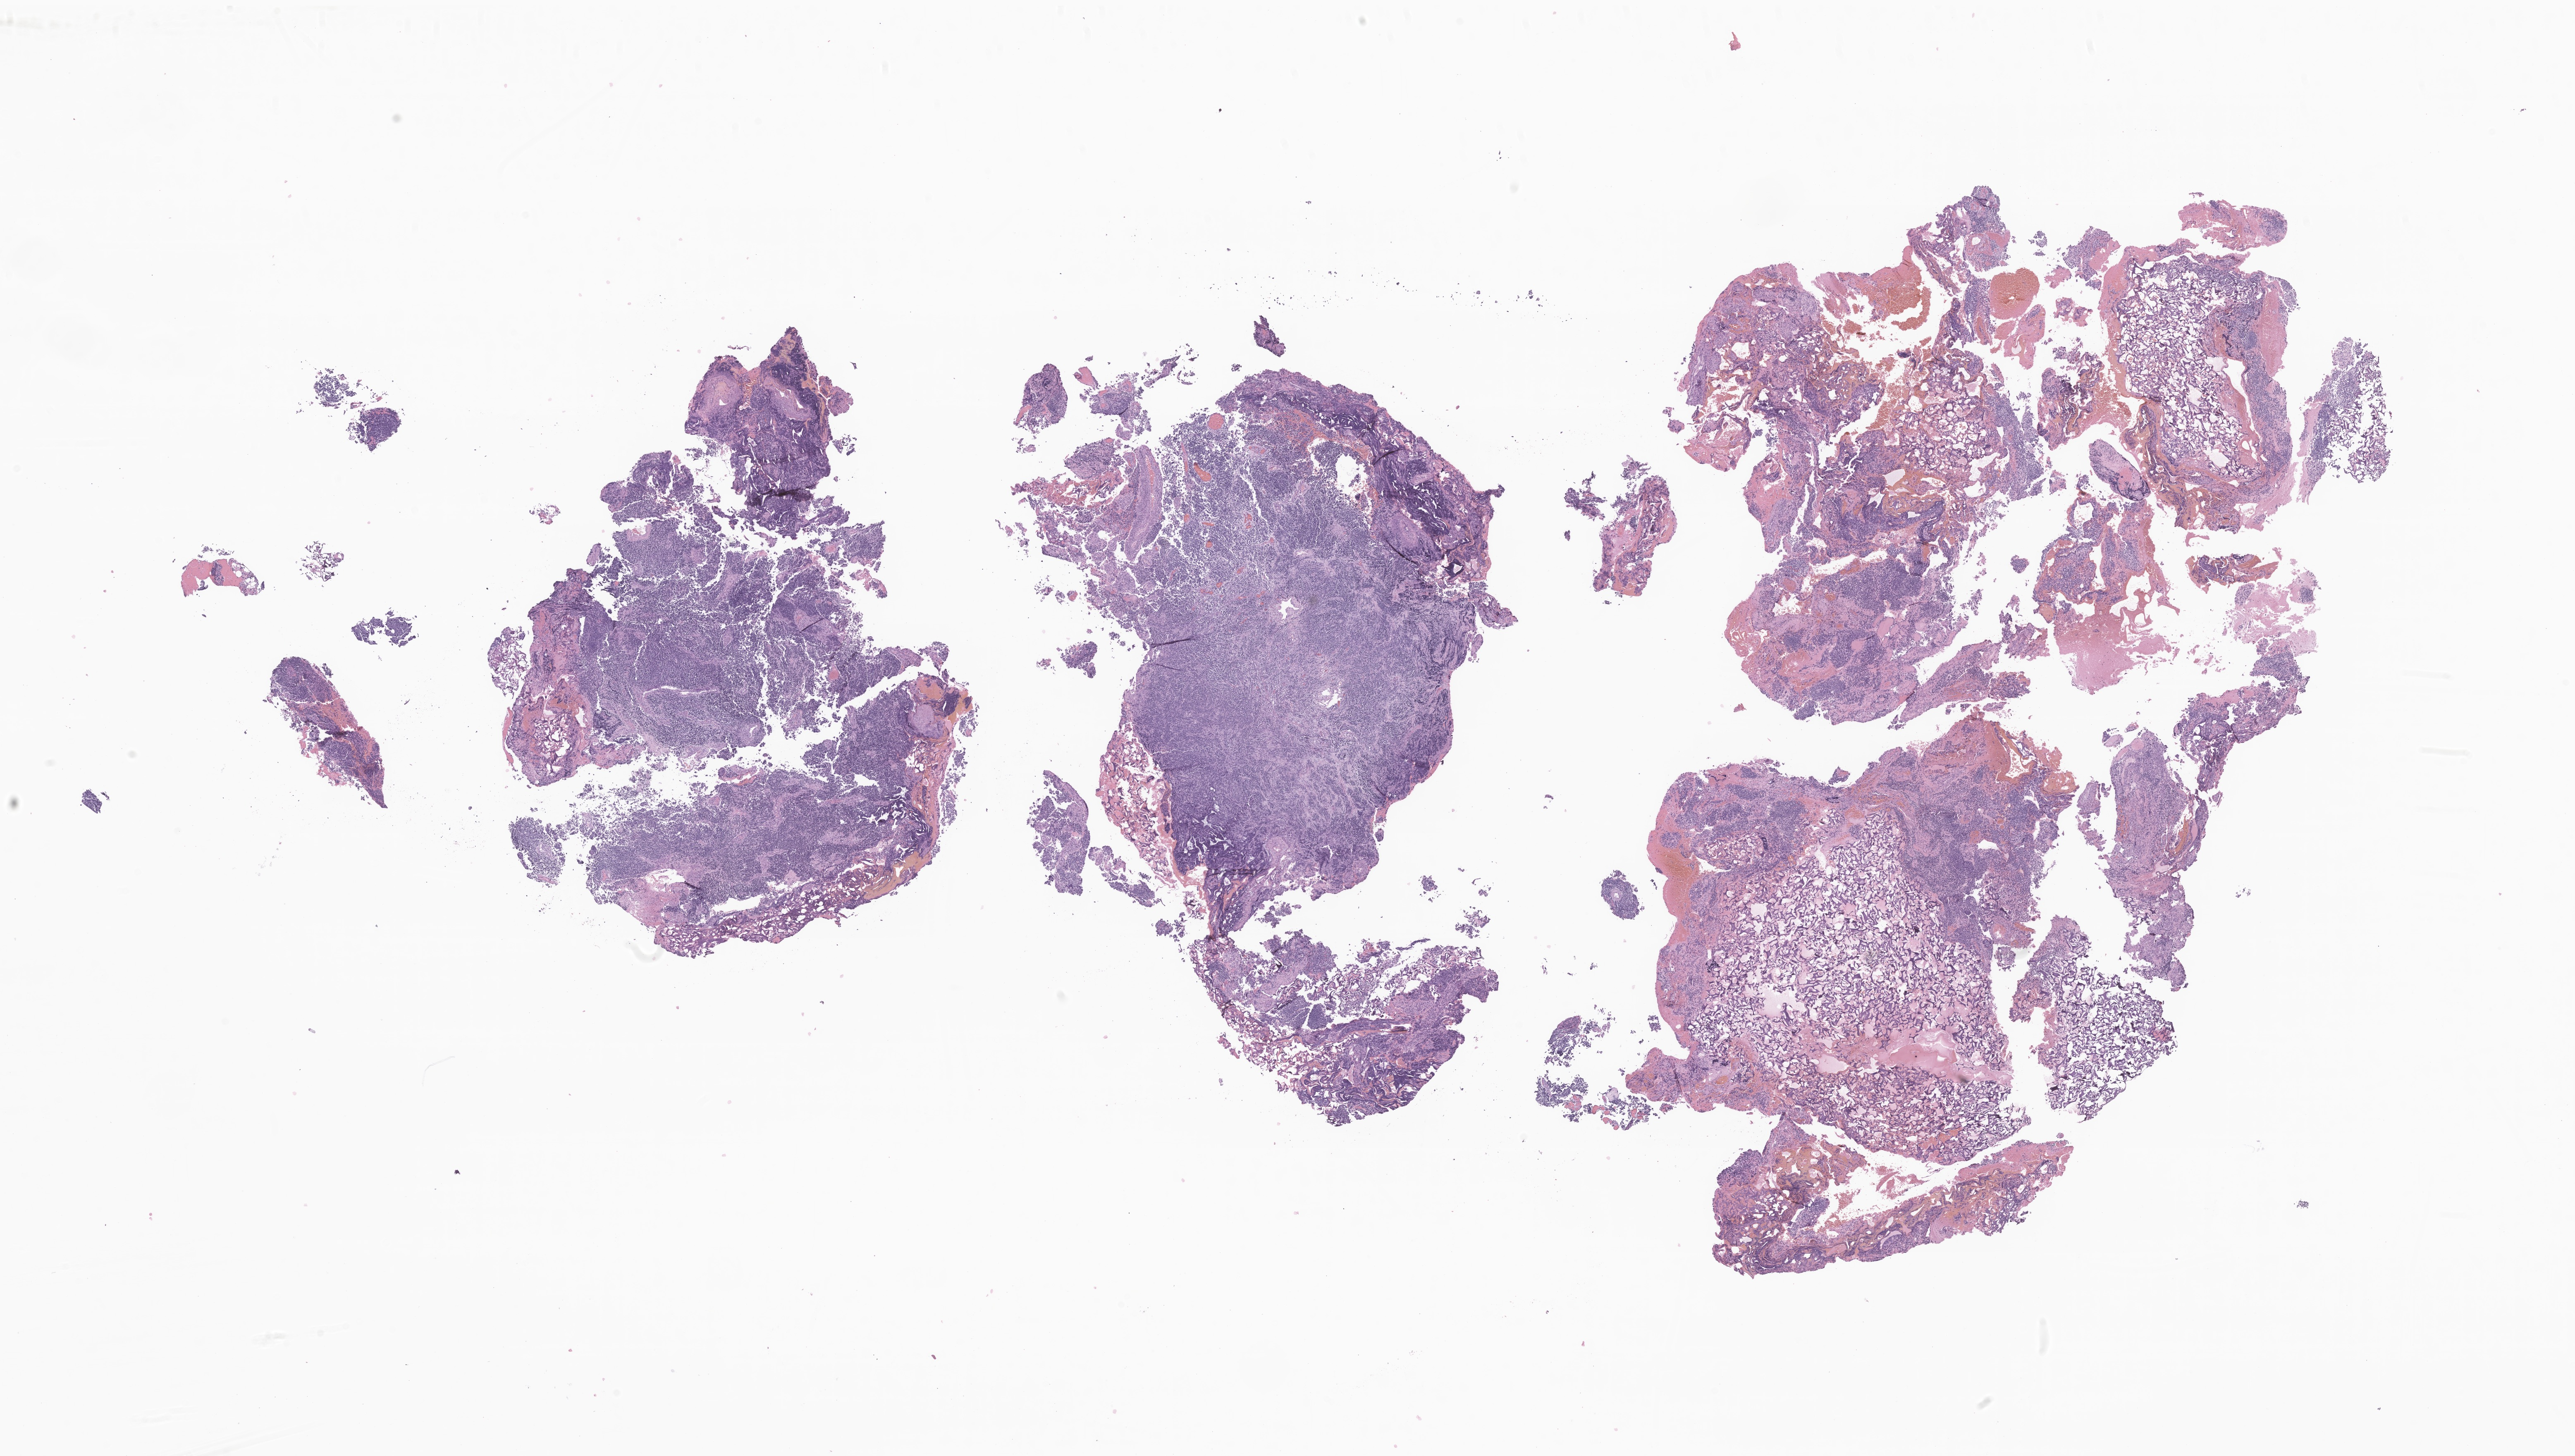
Digitized haematoxylin and eosin-stained section of tumor tissue from the cerebellum, whole scanned area (about 26.3 x 14.8 mm) shown as a low-resolution overview, formalin-fixed paraffin-embedded section. Patient: female, age 66 months.
Diagnosis (ICD-O-3 morphology term): Neoplasm, uncertain whether benign or malignant.